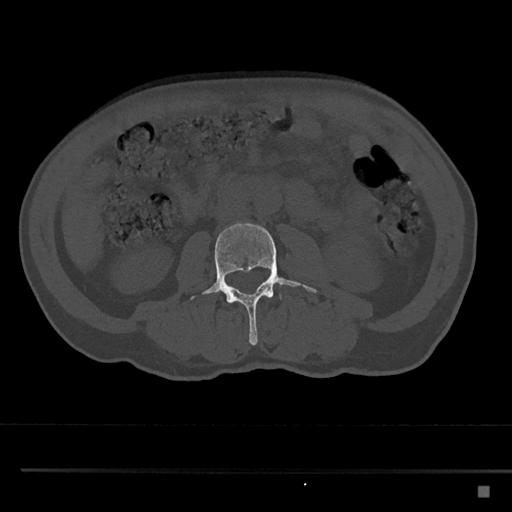
CT including the spine, one axial slice. Position 694 of 797 along the scan axis. Reconstruction kernel Br40s/3. 120 kVp. Bone window (W 1800 / L 400 HU). 512 × 512 image matrix, field of view 391 × 391 mm. Patient: male, 59 years. From the clinical record (not read from this slice): primary cancer: prostate.
Outlined on this slice (semi-automatic segmentation, software-assisted and operator-edited):
- L3 vertebra: bounding box (x1, y1, x2, y2) in pixels: (191, 223, 317, 345)
- L4 vertebra: (280, 294, 282, 300)